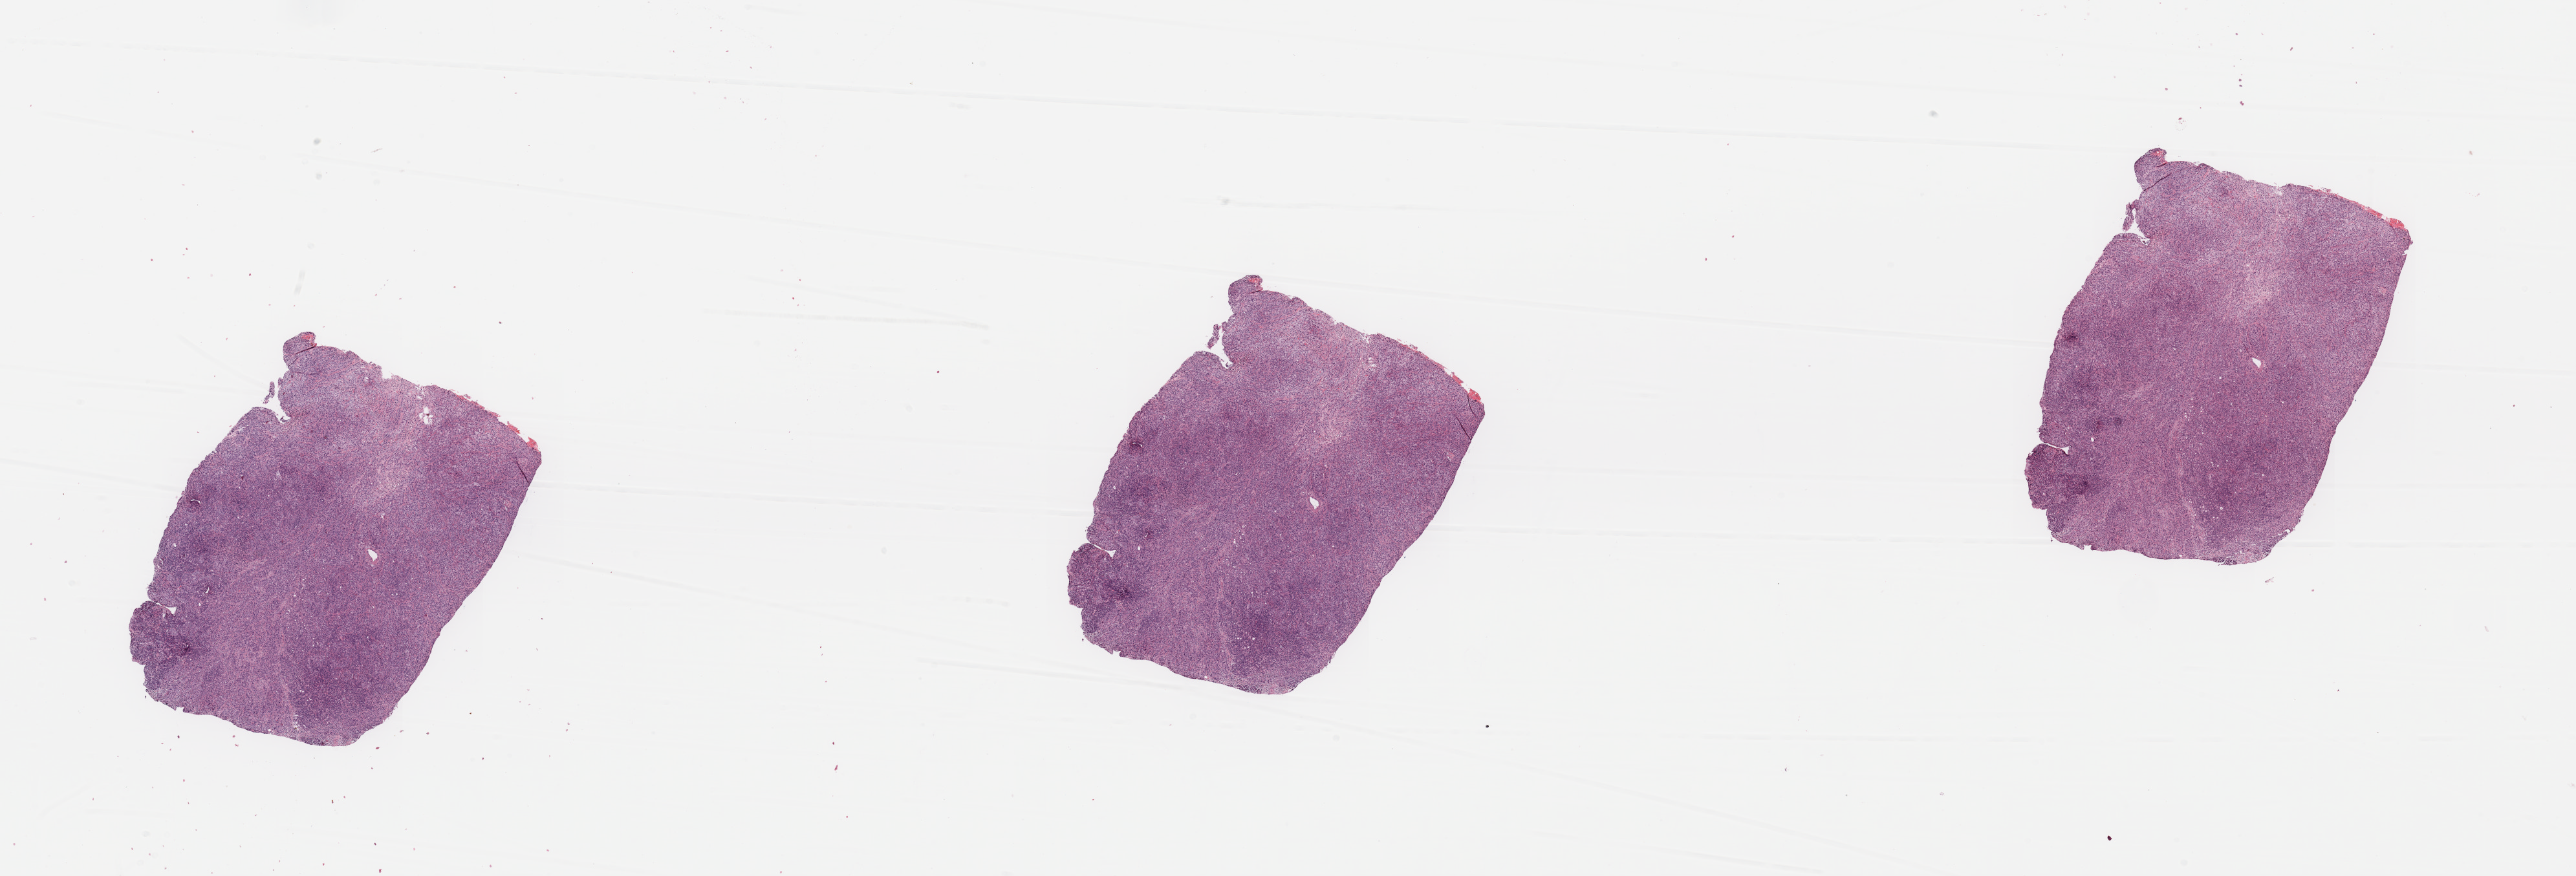
Digitized H&E tissue section (whole slide) — a low-resolution overview of the entire scanned area, about 31.5 x 10.7 mm (from a 20x scan). Tumour tissue sample, sampled site: pancreas. 76-year-old male patient. Histologic grade: G3 (poorly differentiated). Composition of this section per pathologist review: tumour nuclei 50%, necrosis 0%.
- diagnosis: Infiltrating duct carcinoma, NOS
- primary tumour site (as recorded): head
- AJCC pathologic stage: IB